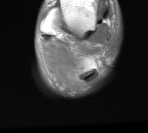
MRI of an extremity soft-tissue mass, one axial slice; slice 8 of 76 in the series (ordered by position); MR volume resampled by the dataset authors to the PET/CT grid (not the native acquisition matrix); 148 × 133 image matrix, field of view 145 × 130 mm. Male patient. Case-level facts recorded for this patient, not image findings: histological type: liposarcoma - round cell; grade: high; site of the primary tumour: right calf.
Annotated regions visible in this slice (expert contour drawn on MRI and transferred to this co-registered scan by the dataset authors):
- gross tumour volume (mass): box from (x=40, y=35) to (x=91, y=91) px